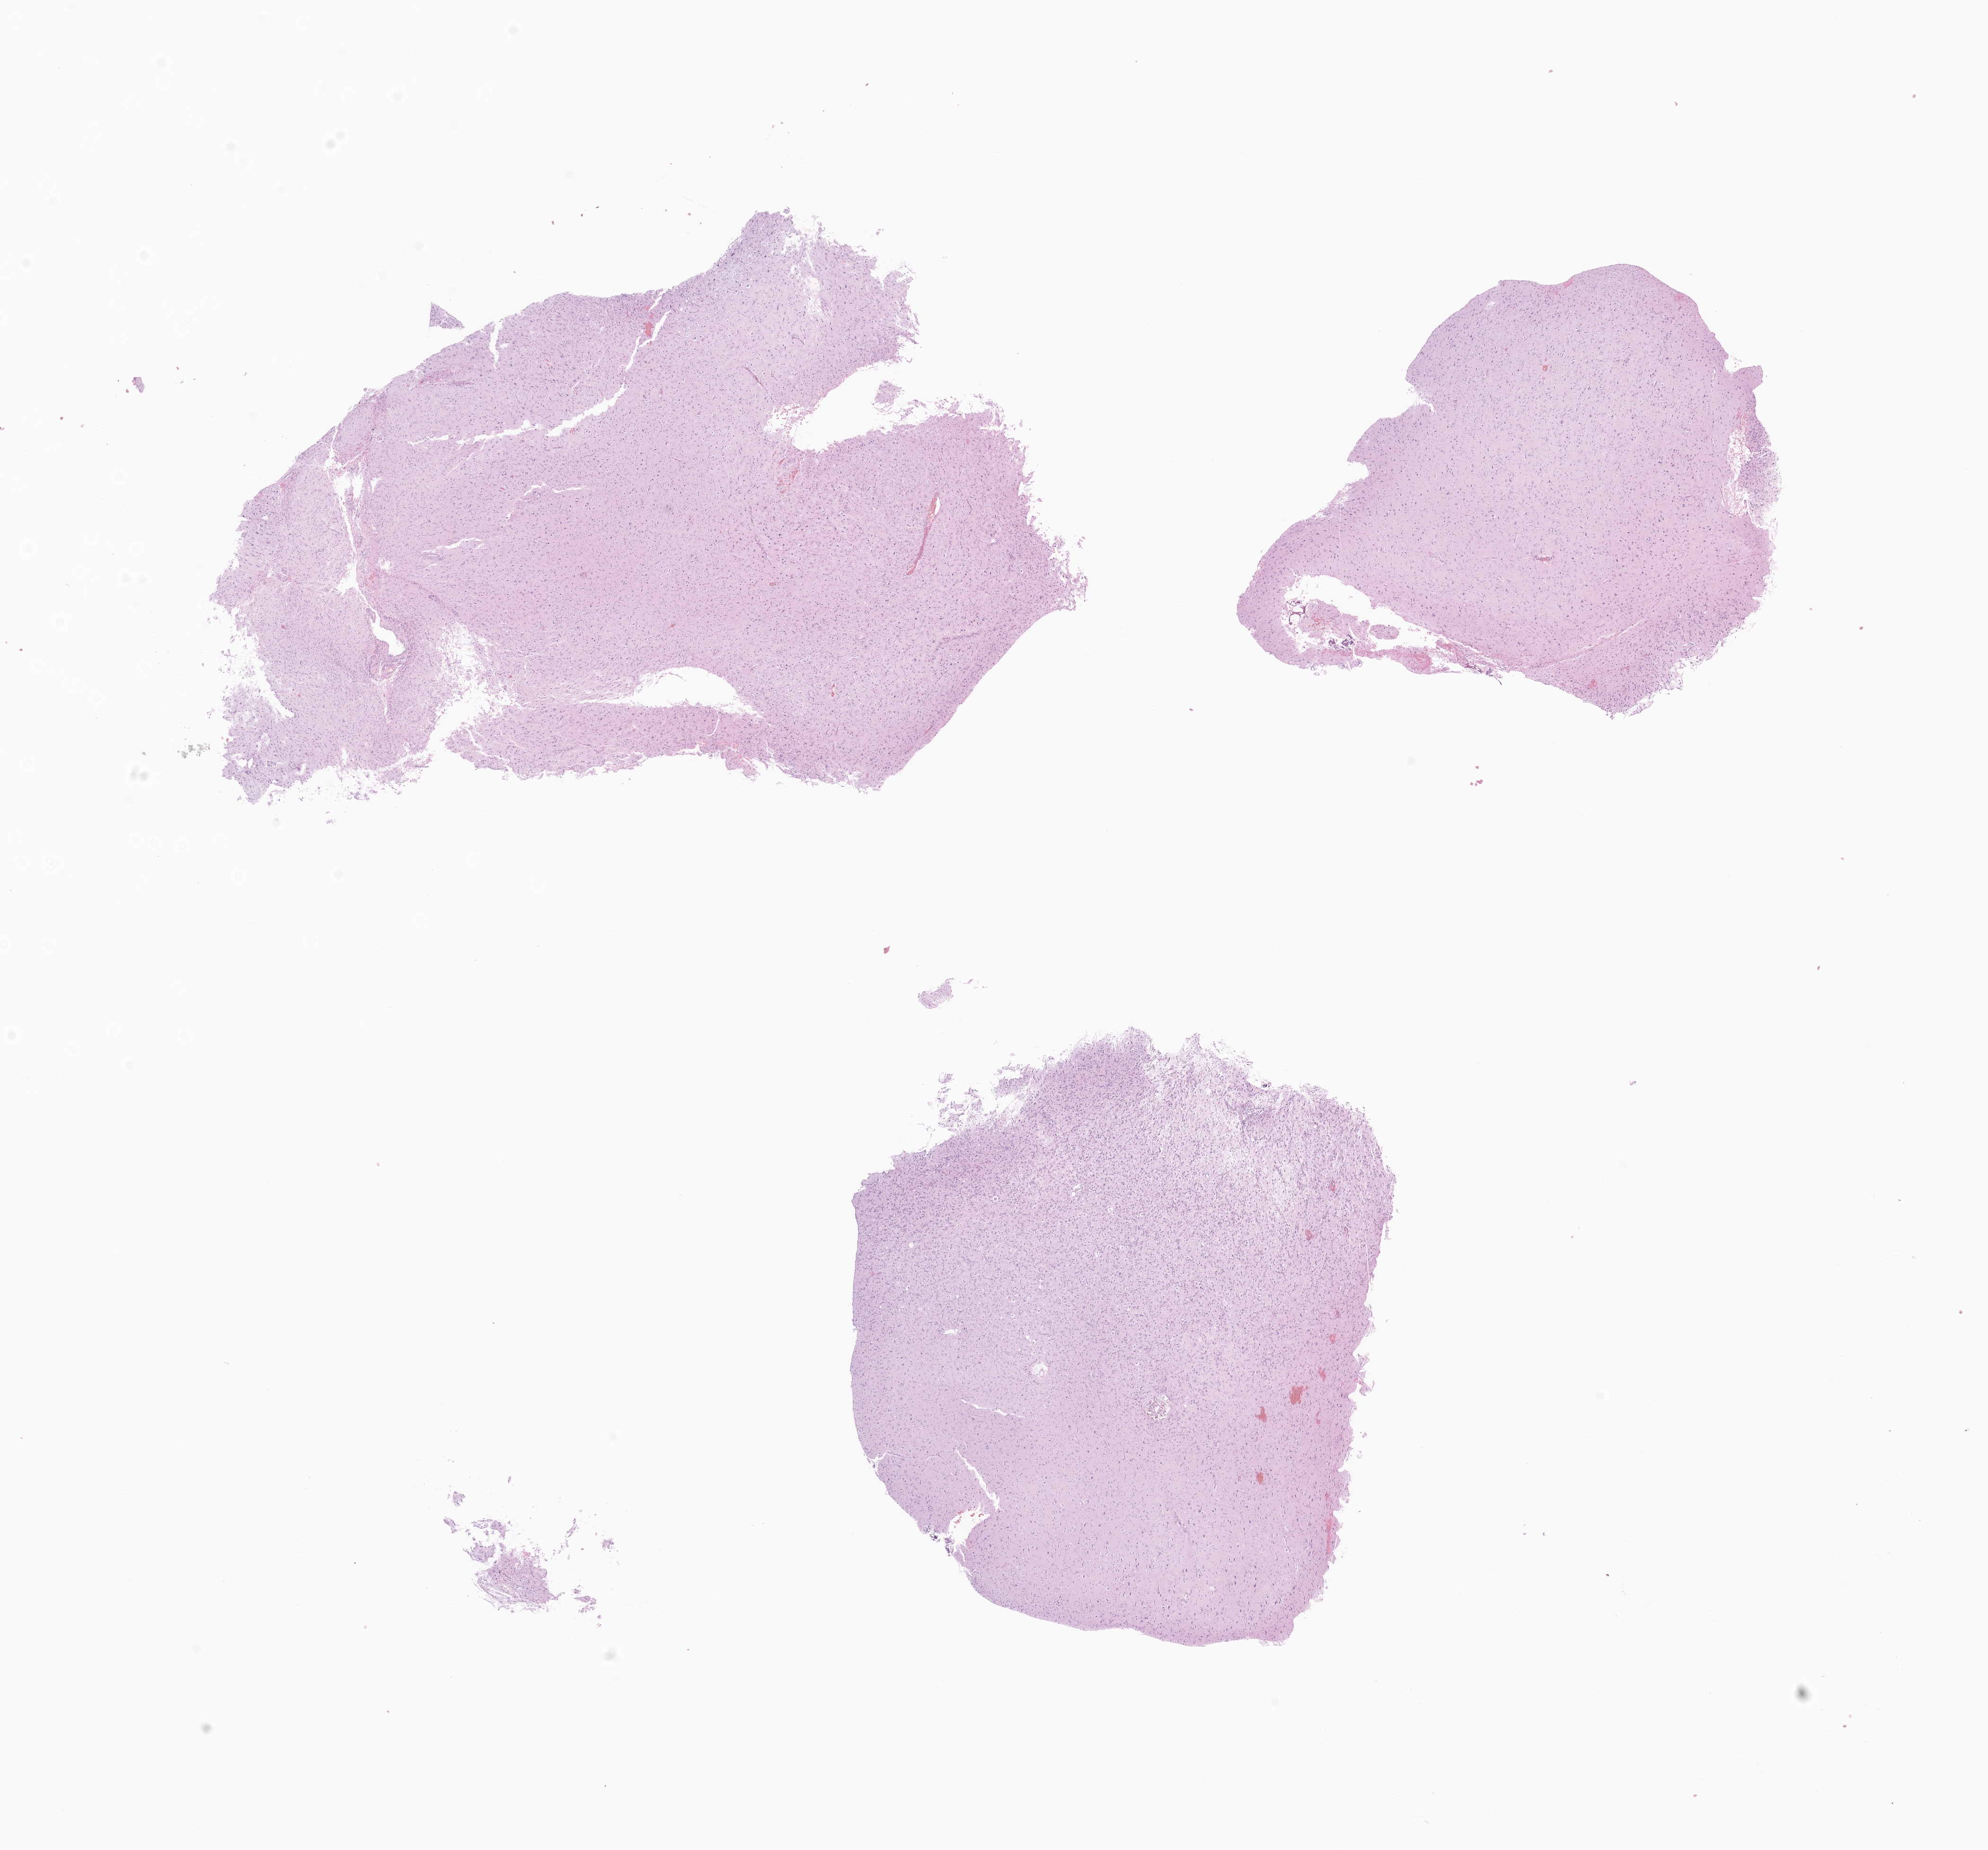
Whole-slide image, H&E stain of tumor tissue from the temporal lobe — low-resolution overview of the scanned area, about 17.7 x 16.5 mm. FFPE section. Patient: male, age 227 months (18 years 11 months).
Recorded diagnosis: Neoplasm, uncertain whether benign or malignant.